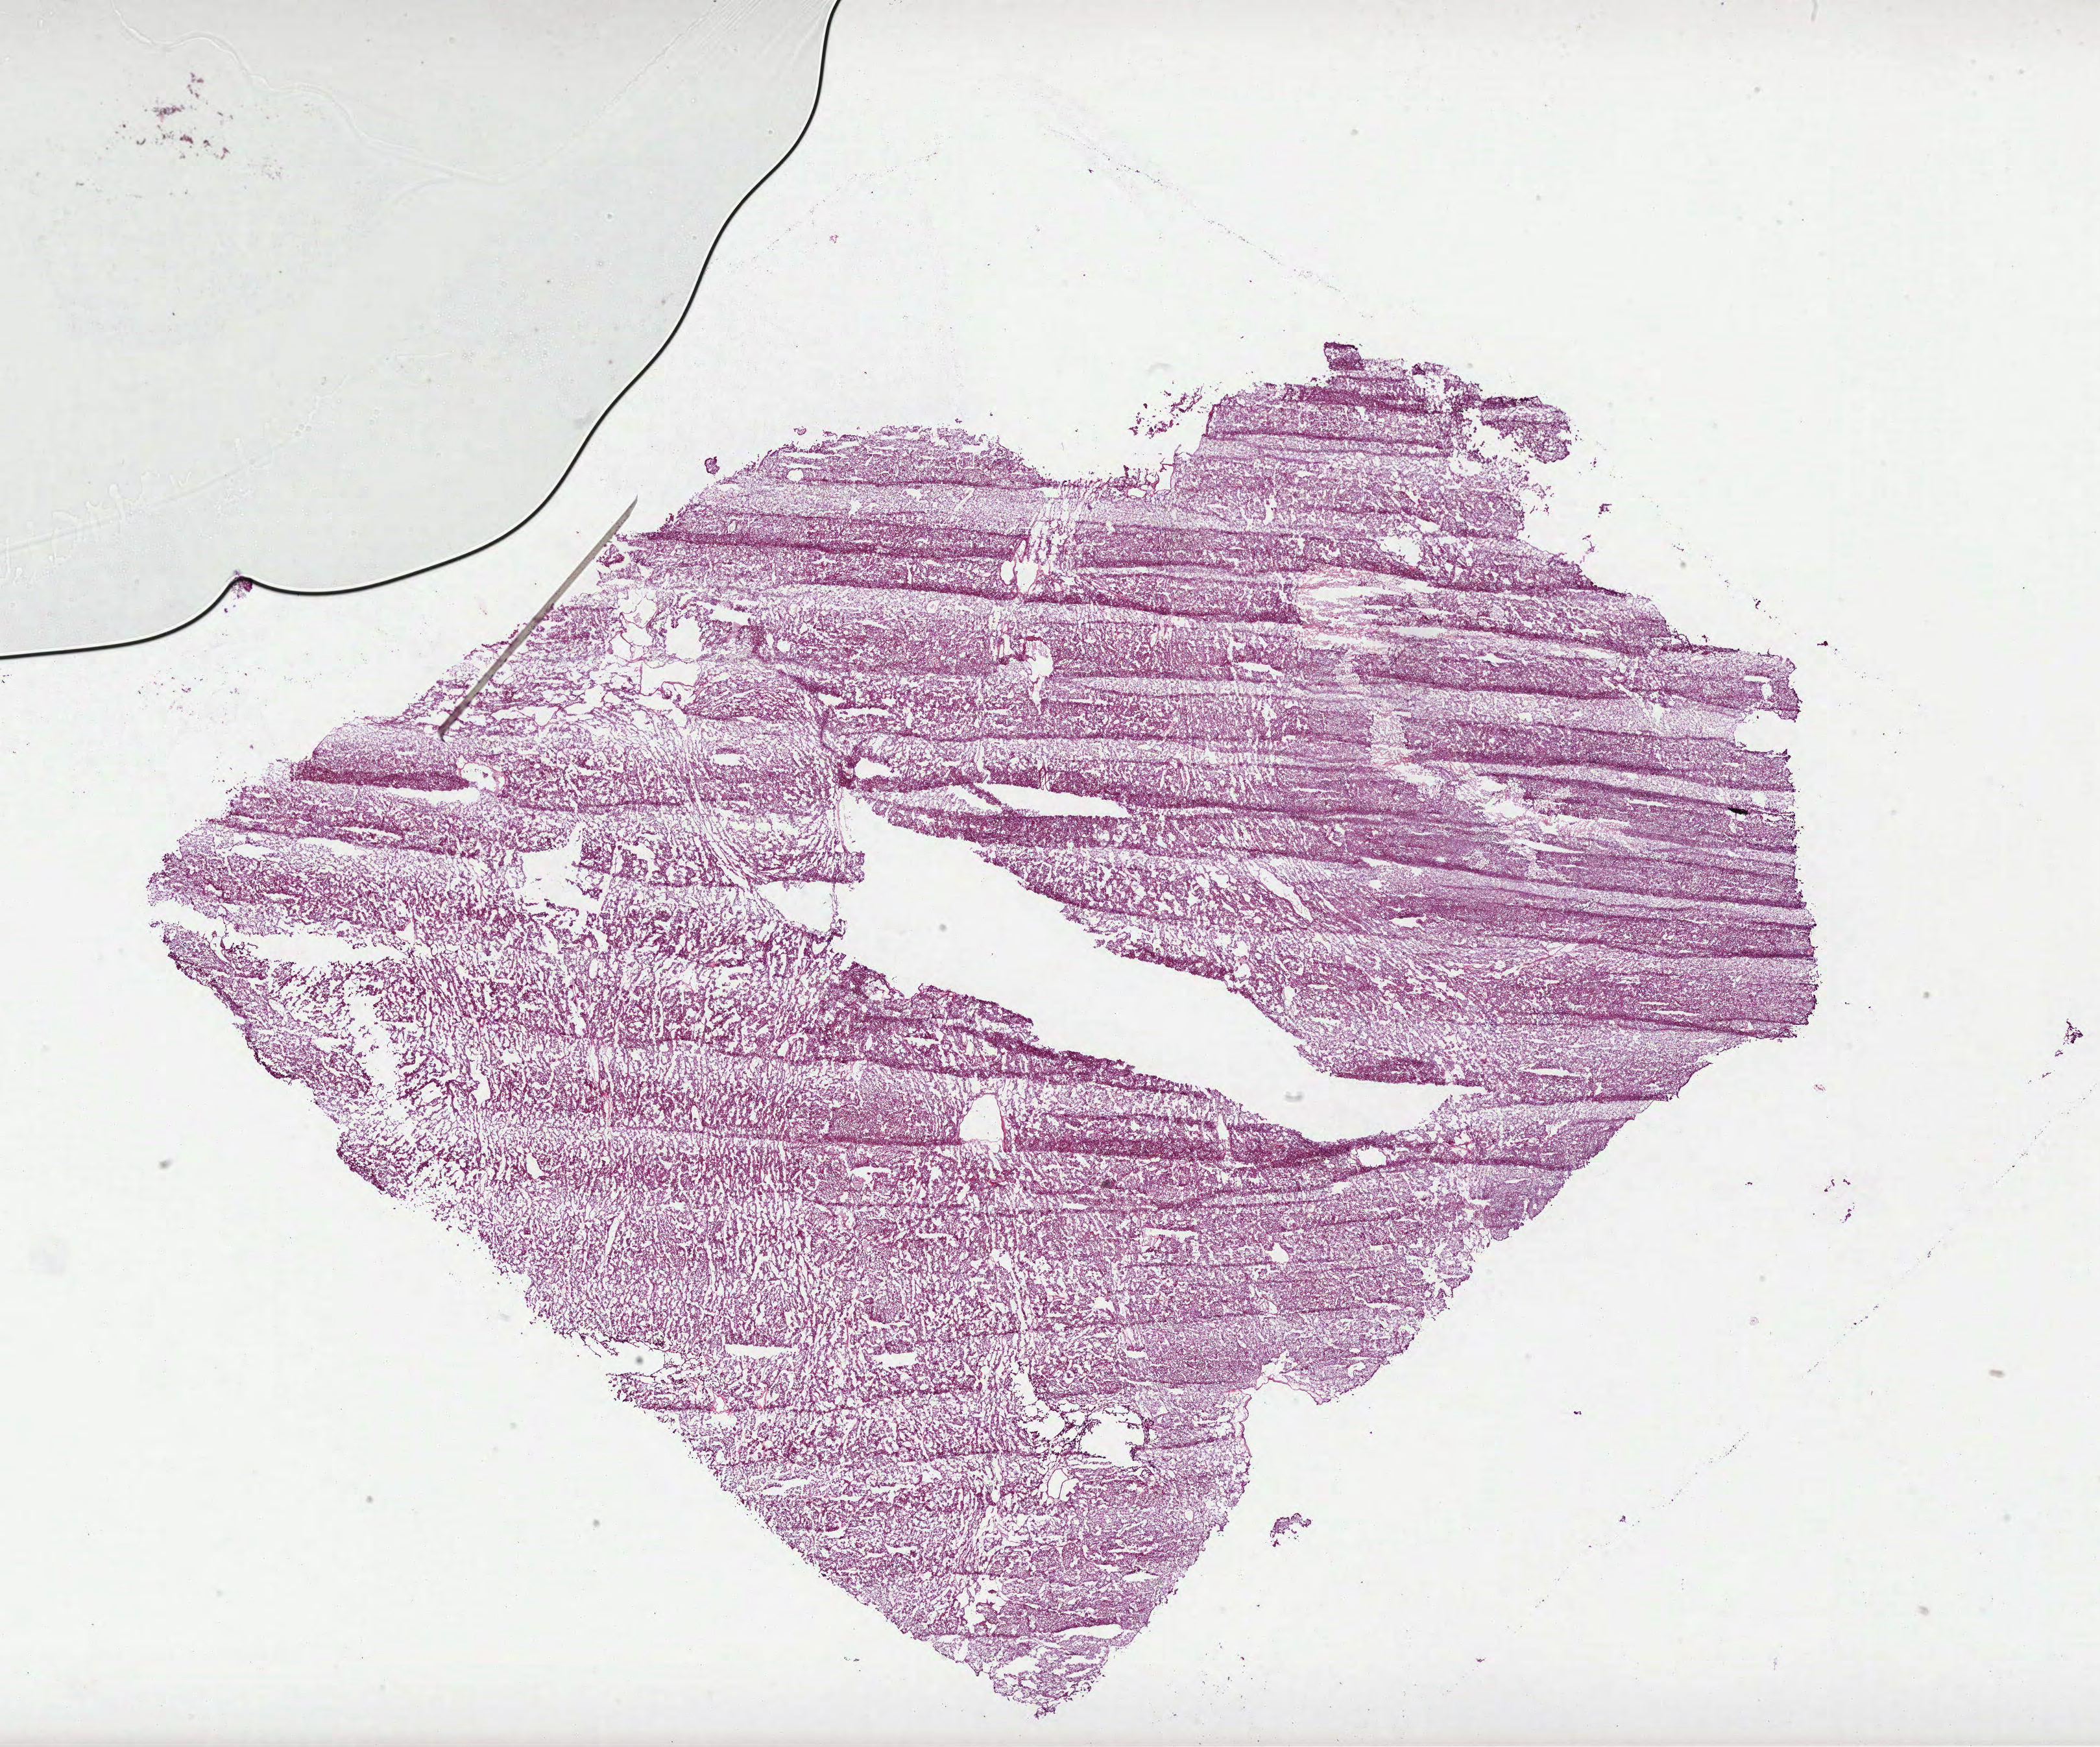
Whole-slide histology image, H&E-stained — a low-resolution overview of the entire scanned area, about 26.1 x 21.7 mm (slide scanned at 40x), frozen section from the bottom of the tissue portion, kidney, primary tumour sample. Female patient; age at initial diagnosis 35 years. Composition of this section per pathologist review: tumour cells 100%, tumour nuclei 95%, normal cells 0%, stromal cells 0%, necrosis 0%. Inflammatory infiltration, as recorded: lymphocyte infiltration 0%, monocyte infiltration 0%, neutrophil infiltration 0%.
AJCC pathologic stage: II (6th edition). Pathologic diagnosis: Renal cell carcinoma, chromophobe type. TNM: T2 NX.